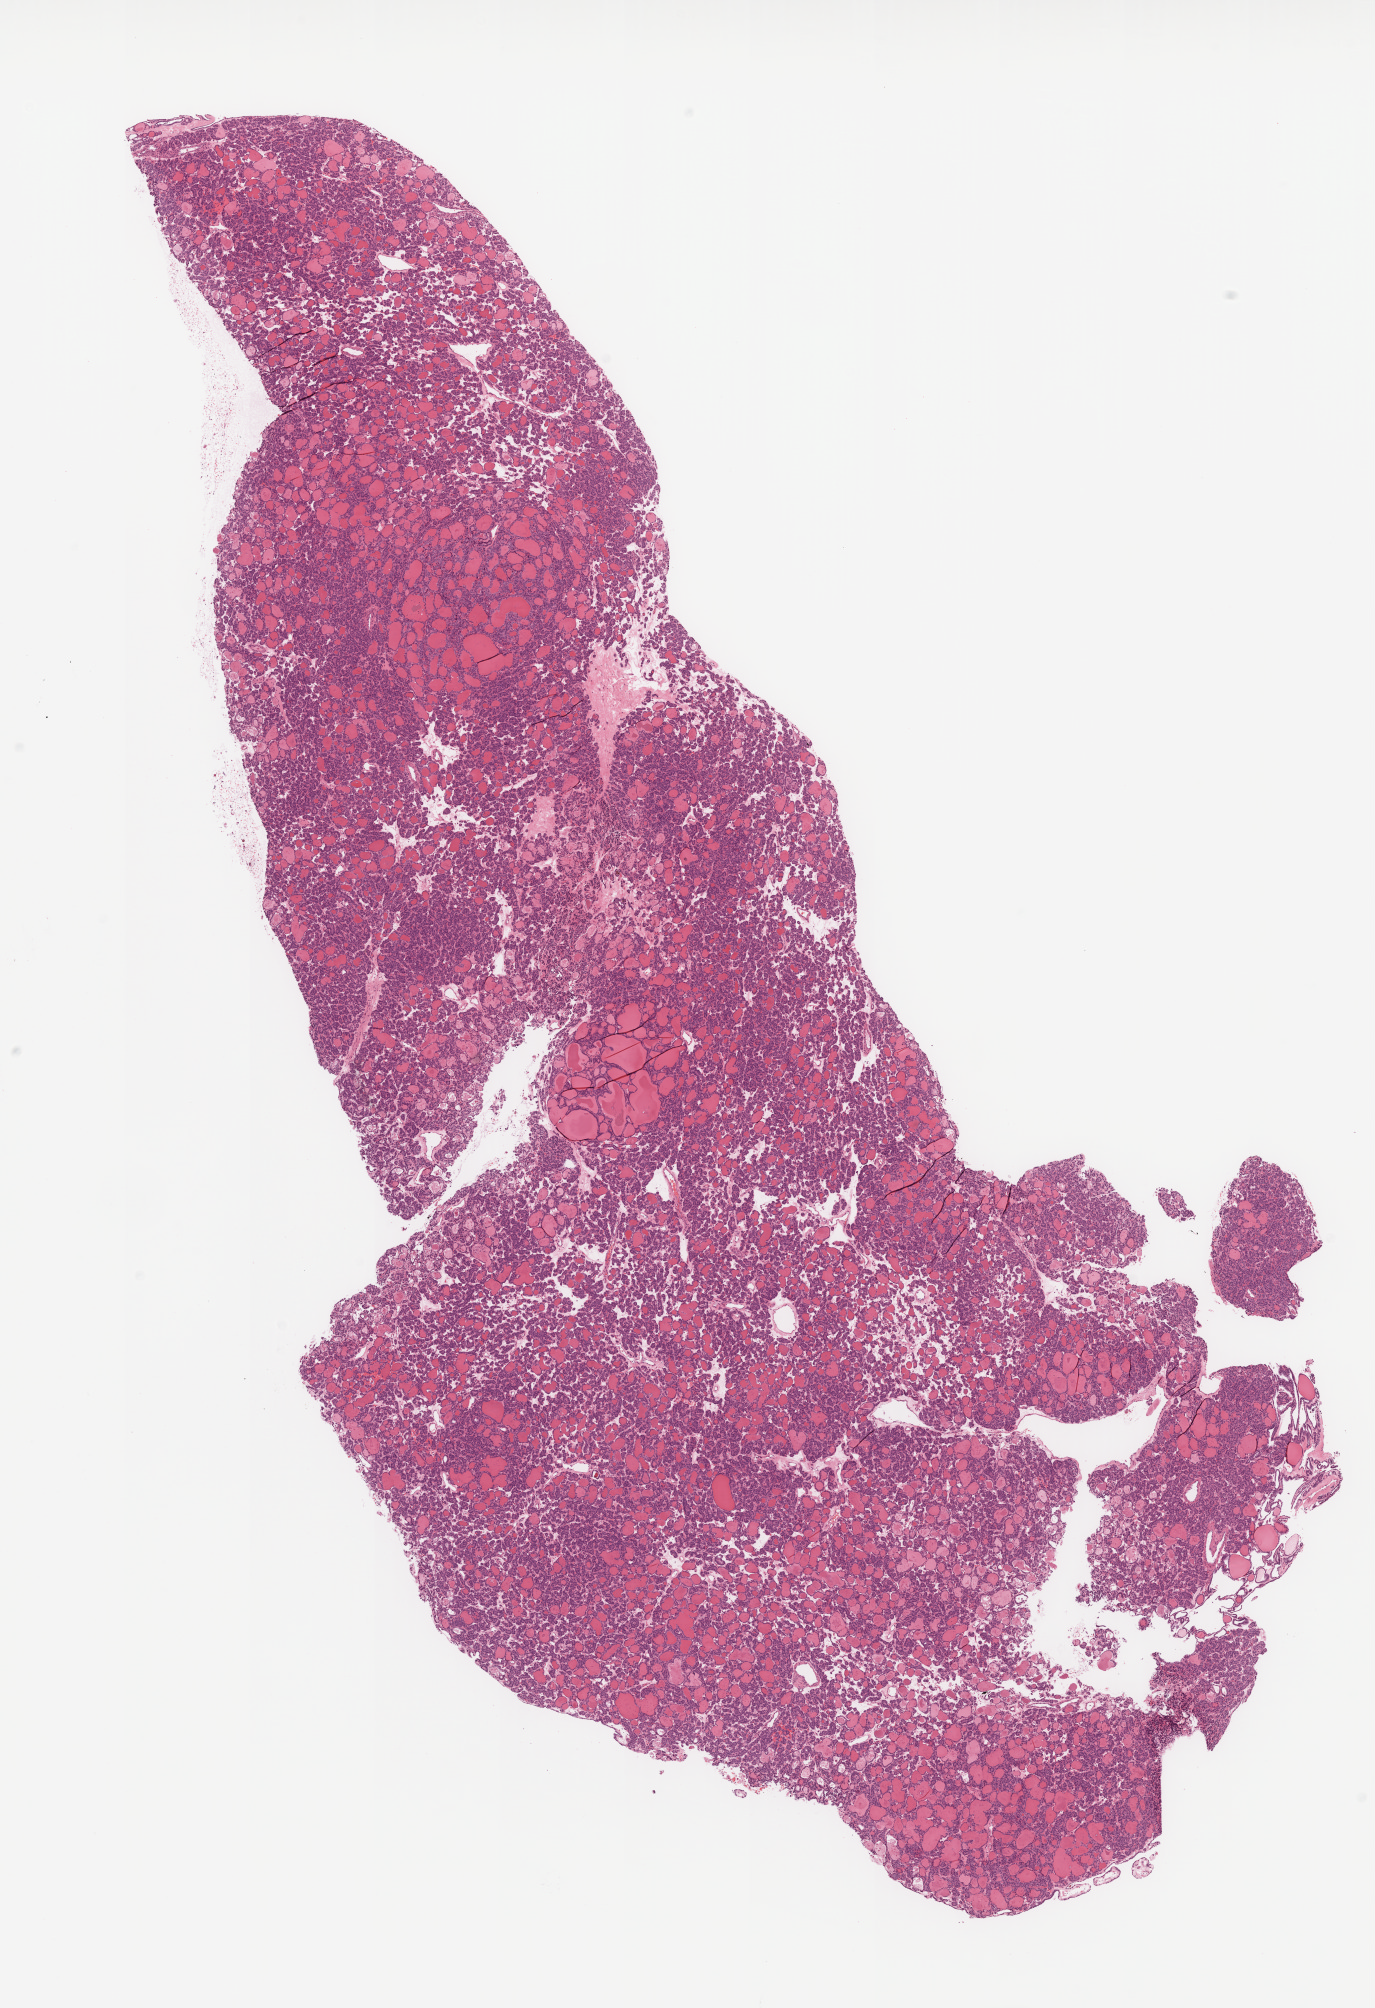
Digitized Hematoxylin and eosin (H&E) stained tissue section (whole slide), a low-resolution overview of the entire scanned area, about 11.0 x 16.1 mm, FFPE section, primary tumour sample from the thyroid. Female, age 33 years at initial diagnosis.
Diagnosis: Papillary carcinoma, follicular variant (thyroid gland). Lymph nodes positive (case pathology): 0 of 3 examined. AJCC pathologic stage: I (7th edition). Laterality: midline.